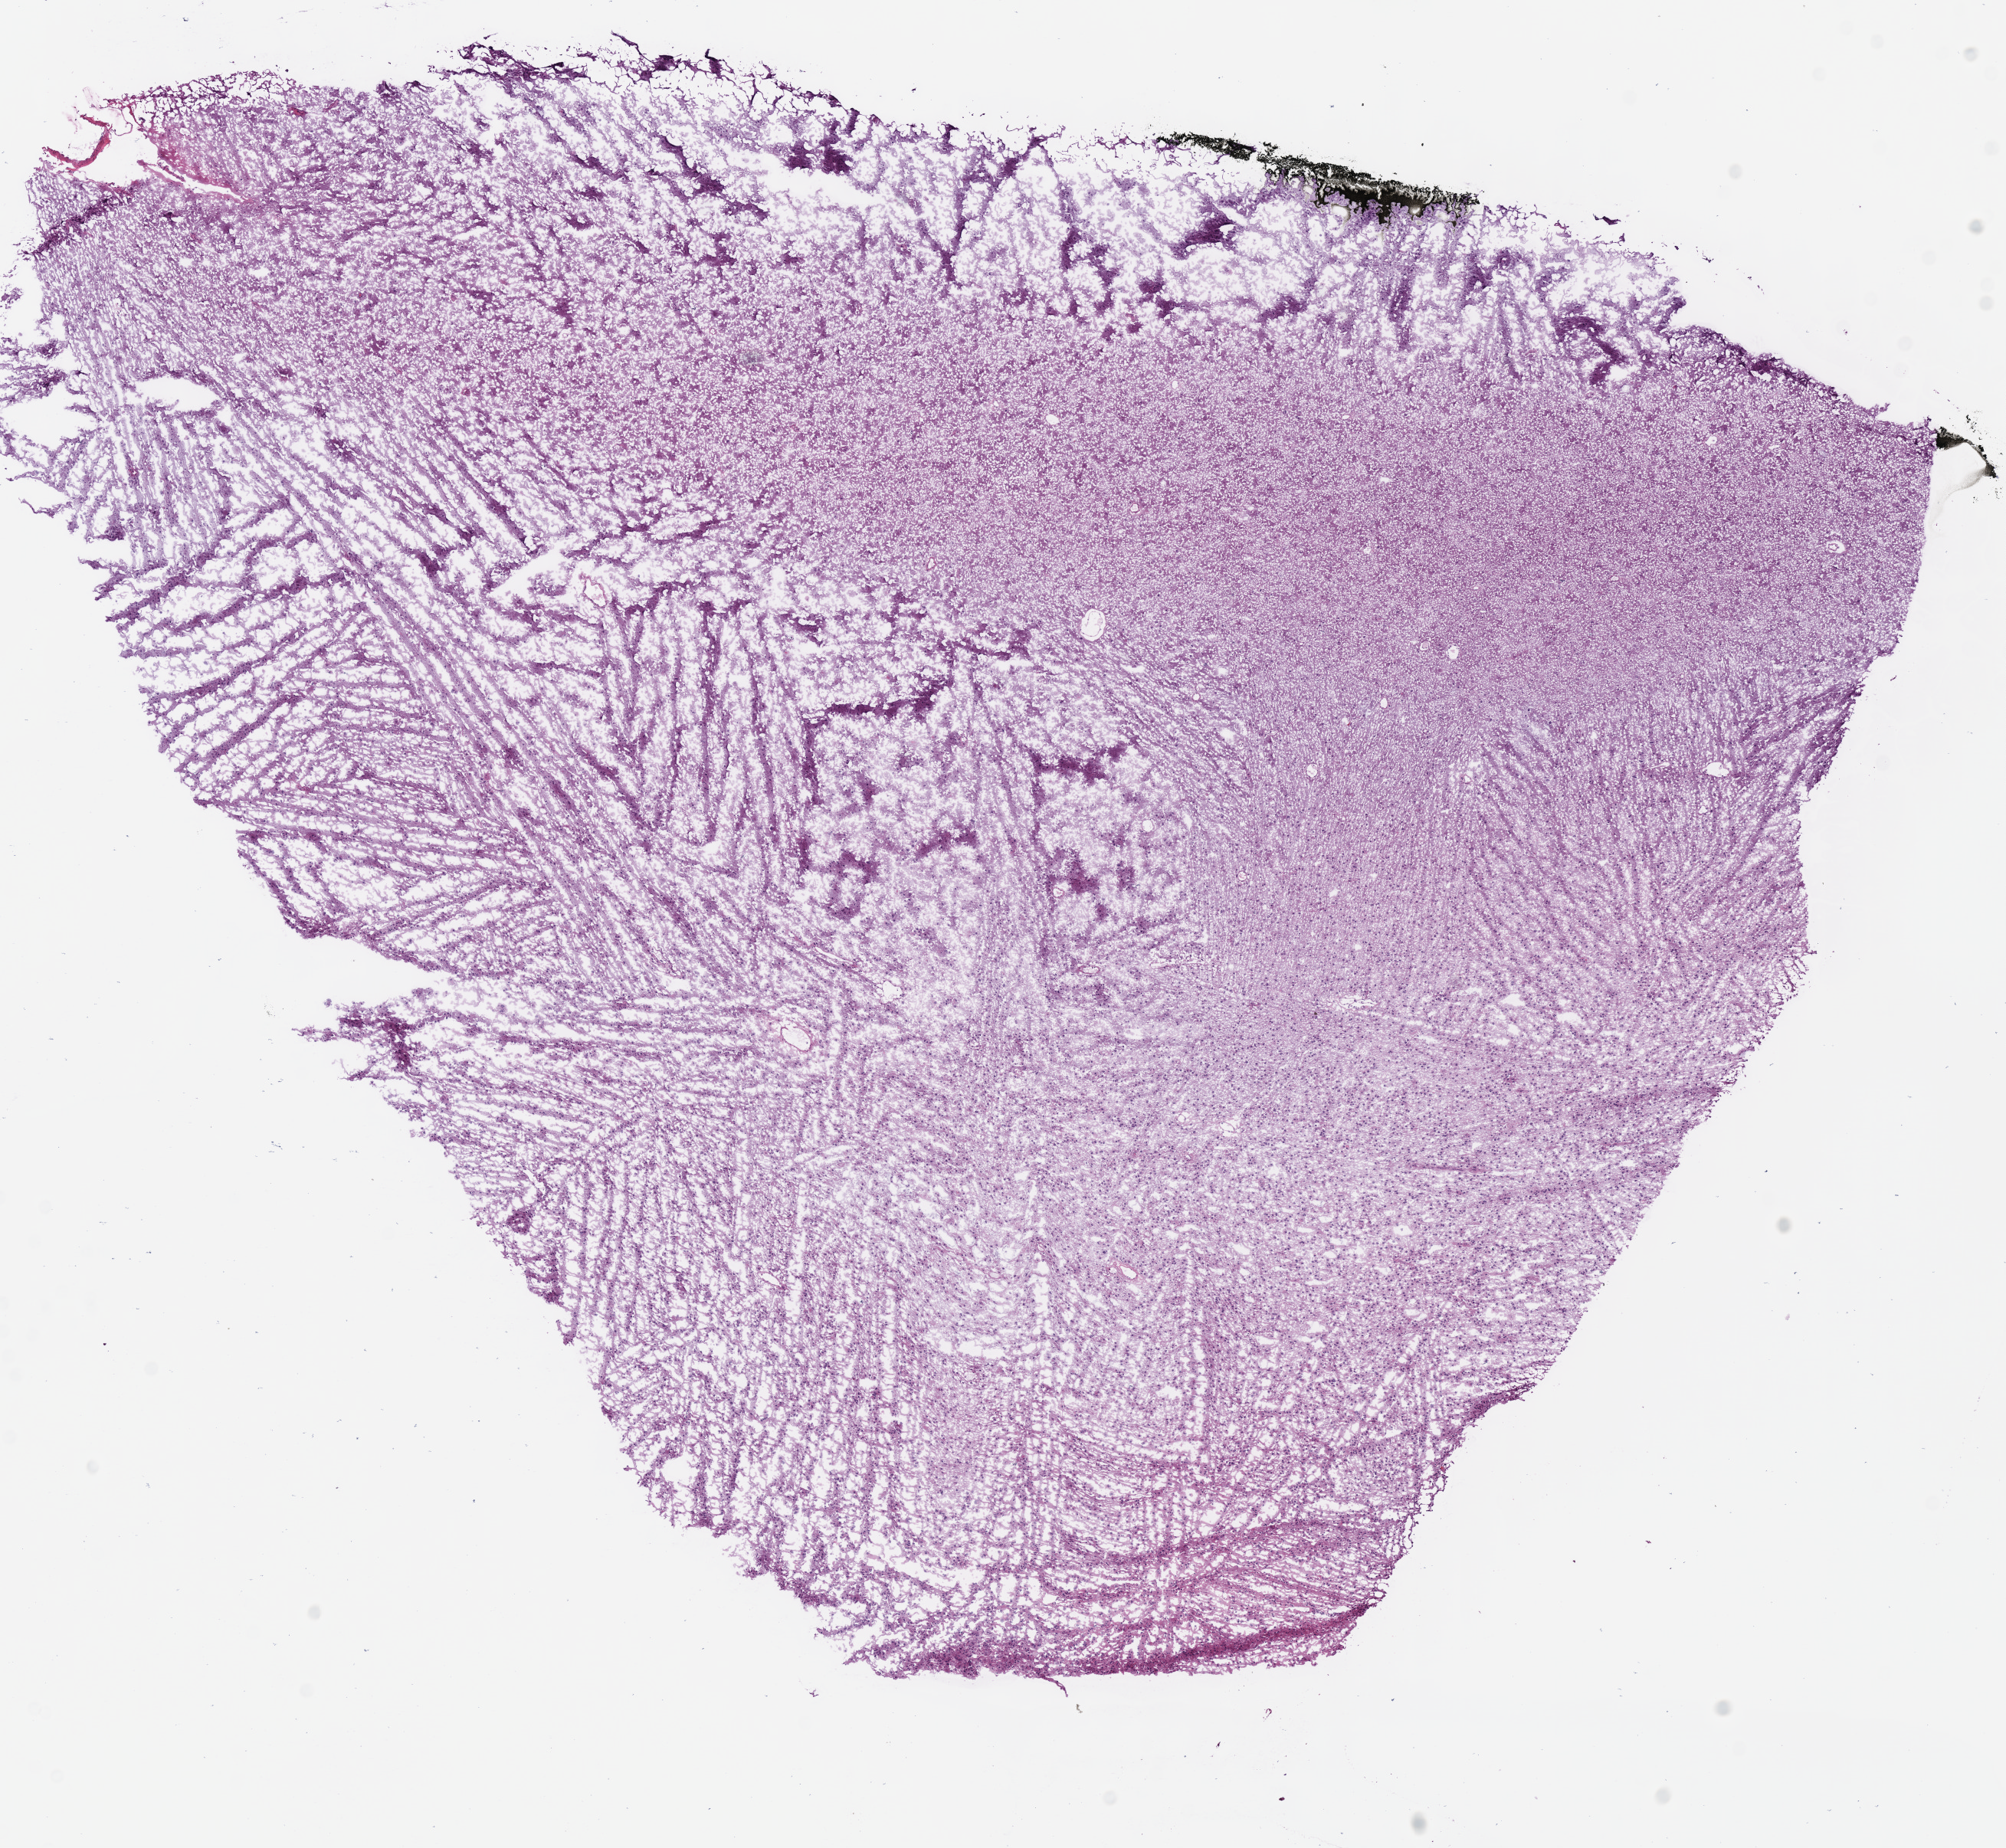
Whole-slide histology image, H&E — a low-resolution overview of the entire scanned area, about 10.3 x 9.5 mm (from a 40x scan). Frozen section from the bottom of the tissue portion. Primary tumour sample from the brain. Female, age 40 years at initial diagnosis. Histologic grade: G2 (moderately differentiated). Slide review estimates, as recorded: tumour cells 100%, tumour nuclei 70%, normal cells 0%, stromal cells 0%, necrosis 0%.
• pathologic diagnosis: Astrocytoma, NOS (cerebrum)
• laterality: right